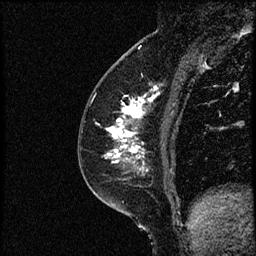
Breast MRI (dynamic contrast-enhanced), one sagittal slice; slice 28 of 52 in the series (ordered by position); dynamic contrast-enhanced study with each time point stored as its own series, time point 2 of 3 at this slice position (early post-contrast, ordered by acquisition time); 1.5 T; TE 4.2 ms, TR 17.6 ms; 256 × 256 image matrix, field of view 200 × 200 mm. Patient: female, 49 years. Case-level facts recorded for this patient, not image findings: setting: breast cancer imaged before/during neoadjuvant chemotherapy; receptor status: HER2-positive.
Structures marked on this image (semi-automatic segmentation, software-assisted and operator-edited):
- analysis volume of interest (the breast-tissue region the enhancement analysis was run in; not a lesion): box from (x=85, y=65) to (x=182, y=175) px
- tumour enhancement mask (voxels above the 100 % enhancement threshold inside the analysis volume of interest): (x=106, y=87)–(x=159, y=170)